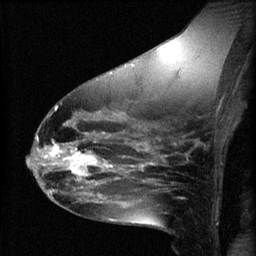
Breast MRI (dynamic contrast-enhanced), one sagittal slice; slice 34 of 60 in the series (ordered by position); 3 images stored at this slice position (order not interpretable as contrast timing); 1.5 T; TE 4.2 ms, TR 8.2 ms; 2 mm slice thickness; 256 × 256 image matrix, field of view 180 × 180 mm. Female patient, age 49 years.
Annotated regions visible in this slice (semi-automatically segmented with operator editing):
- analysis volume of interest (the breast-tissue region the enhancement analysis was run in; not a lesion): bounding box [x1, y1, x2, y2] px = [45, 136, 109, 187]
- tumour enhancement mask (voxels above the 70 % enhancement threshold inside the analysis volume of interest): [45, 140, 109, 187]